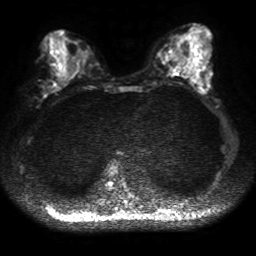
Breast MRI, one axial slice; position 21 of 50 along the scan axis; diffusion-weighted series; image 2 of 4 stored at this slice position (different b-values; order by instance number); 1.5 T; 256 × 256 image matrix, field of view 320 × 320 mm. Female patient.
Structures marked on this image (expert manual segmentation):
- tumour on diffusion-weighted imaging: bounding box <53,83,61,92> (left, top, right, bottom; pixels)